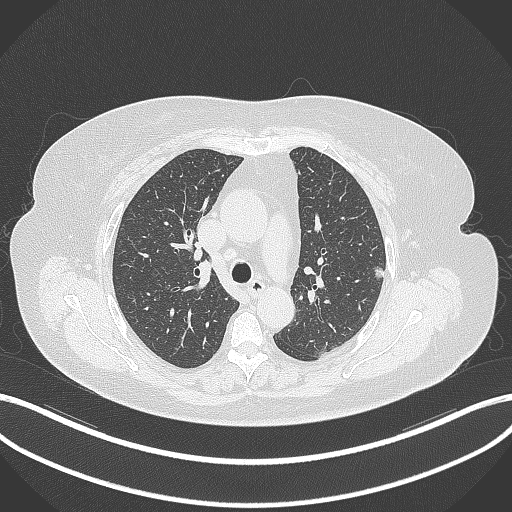
Chest CT, one axial slice; position 219 of 309 along the scan axis; 120 kVp; lung window (W 1500 / L -600 HU); 1 mm slice thickness; 512 × 512 image matrix. Female patient, age 70 years. Case-level facts recorded for this patient, not image findings: clinical TNM (as recorded): T1c N0 M0.
Annotated regions visible in this slice (rectangle marked by the reading radiologist):
- lung tumour (recorded histology: adenocarcinoma): bounding box (x1, y1, x2, y2) in pixels: (375, 261, 386, 282)